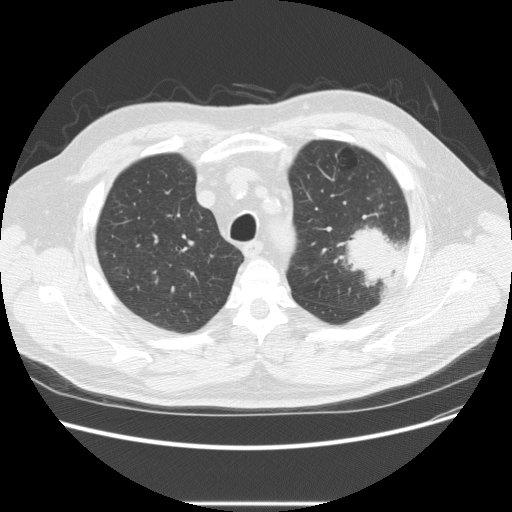
Low-dose screening chest CT, axial slice. First (baseline) screen. Lung window (W 1500 / L -600 HU). Slice 55 of 233 in the series. Male, age 73 years at enrolment. Former smoker at enrolment.
Expert reader's lesion annotation, bounding box <332,215,413,285> (left, top, right, bottom; pixels). The screening reader recorded 2 non-calcified nodules or masses ≥4 mm on this exam (left upper lobe, right upper lobe); which of them this box marks is not recorded. Official screen result: positive, change unspecified: nodule(s) >= 4 mm or enlarging nodule(s), mass(es), or other non-specific abnormalities suspicious for lung cancer. Participant outcome: lung cancer diagnosed 11 days after this screen — bronchiolo-alveolar adenocarcinoma, NOS, other location, well differentiated (G1), stage IV (AJCC 6th edition).